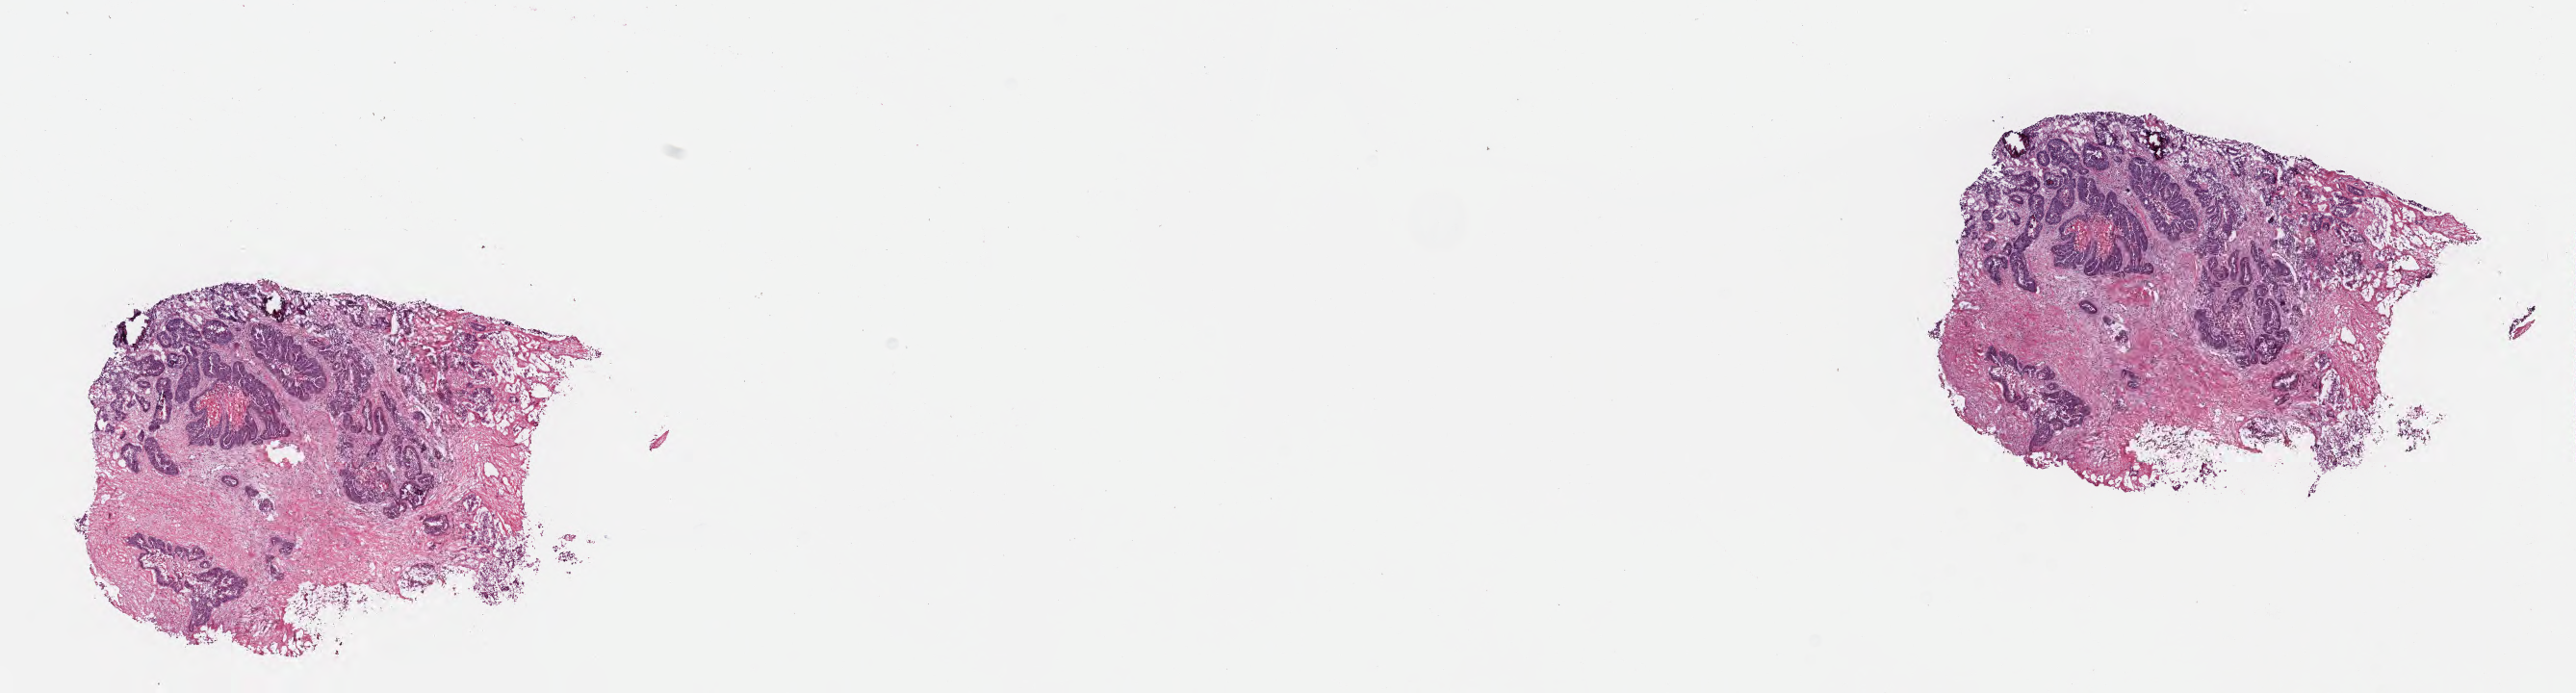
Whole-slide image, hematoxylin and eosin (H&E) stain — low-resolution overview of the scanned area, about 21.6 x 5.8 mm, cryosection, metastatic tumor tissue, resected from liver. Male, age 56 years at initial diagnosis. Pathologist review of this section (percent, as recorded): tumor cells 85%, tumor nuclei 85%, stromal cells 12%, necrosis 3%, normal cells 0%. Infiltration values recorded for this section: lymphocyte infiltration 3%, monocyte infiltration 1%, neutrophil infiltration 4%.
Section: top of the tissue portion. Patient diagnosis (primary): Adenocarcinoma, metastatic, NOS.